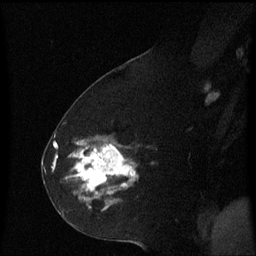
Breast MRI (dynamic contrast-enhanced), one sagittal slice; position 31 of 60 along the scan axis; dynamic contrast-enhanced series, image 2 of 3 at this slice position (ordered by acquisition); 1.5 T; TE 4.2 ms, TR 8.4 ms; 2.2 mm slice thickness; 256 × 256 image matrix. Female patient, age 60 years. From the clinical record (not read from this slice): setting: breast cancer imaged before/during neoadjuvant chemotherapy; receptor status: triple-negative.
Outlined on this slice (semi-automatically segmented with operator editing):
- analysis volume of interest (the breast-tissue region the enhancement analysis was run in; not a lesion): bounding box <69,142,139,213> (left, top, right, bottom; pixels)
- tumour enhancement mask (voxels above the 70 % enhancement threshold inside the analysis volume of interest): <70,144,138,195>